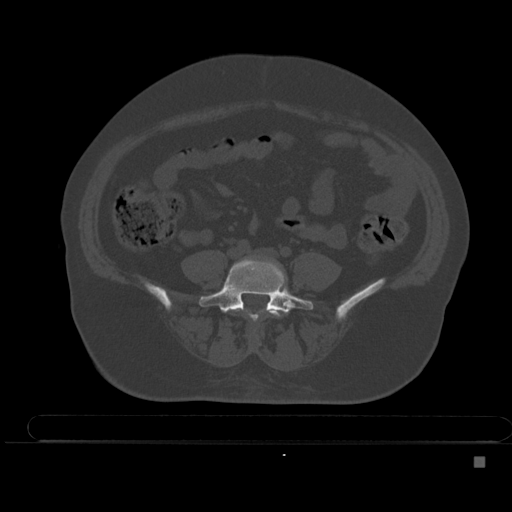
CT including the spine, one axial slice. Position 115 of 495 along the scan axis. Bone window (W 1800 / L 400 HU). 1.5 mm slice thickness. 512 × 512 image matrix, field of view 404 × 404 mm. Female patient, age 33 years. Case-level facts recorded for this patient, not image findings: primary cancer: breast; vertebrae with lytic lesions (as recorded): T1.
Annotated regions visible in this slice (semi-automatic segmentation, software-assisted and operator-edited):
- L4 vertebra: bounding box (x1, y1, x2, y2) in pixels: (235, 309, 281, 340)
- L5 vertebra: (199, 259, 314, 320)